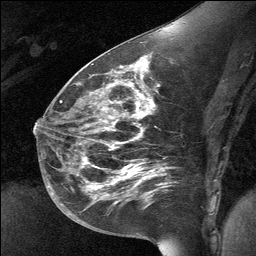
Breast MRI (dynamic contrast-enhanced), one sagittal slice. Slice 33 of 64 in the series (ordered by position). Dynamic contrast-enhanced study with each time point stored as its own series, time point 2 of 3 at this slice position (early post-contrast, ordered by acquisition time). 1.5 T. TE 4.8 ms, TR 27 ms. 2 mm slice thickness. 256 × 256 image matrix, field of view 200 × 200 mm. Patient: female, 39 years. From the clinical record (not read from this slice): setting: breast cancer imaged before/during neoadjuvant chemotherapy; receptor status: HER2-positive.
Outlined on this slice (semi-automatic segmentation, software-assisted and operator-edited):
- analysis volume of interest (the breast-tissue region the enhancement analysis was run in; not a lesion): box from (x=70, y=69) to (x=165, y=224) px
- tumour enhancement mask (voxels above the 90 % enhancement threshold inside the analysis volume of interest): (x=113, y=177)–(x=146, y=183)